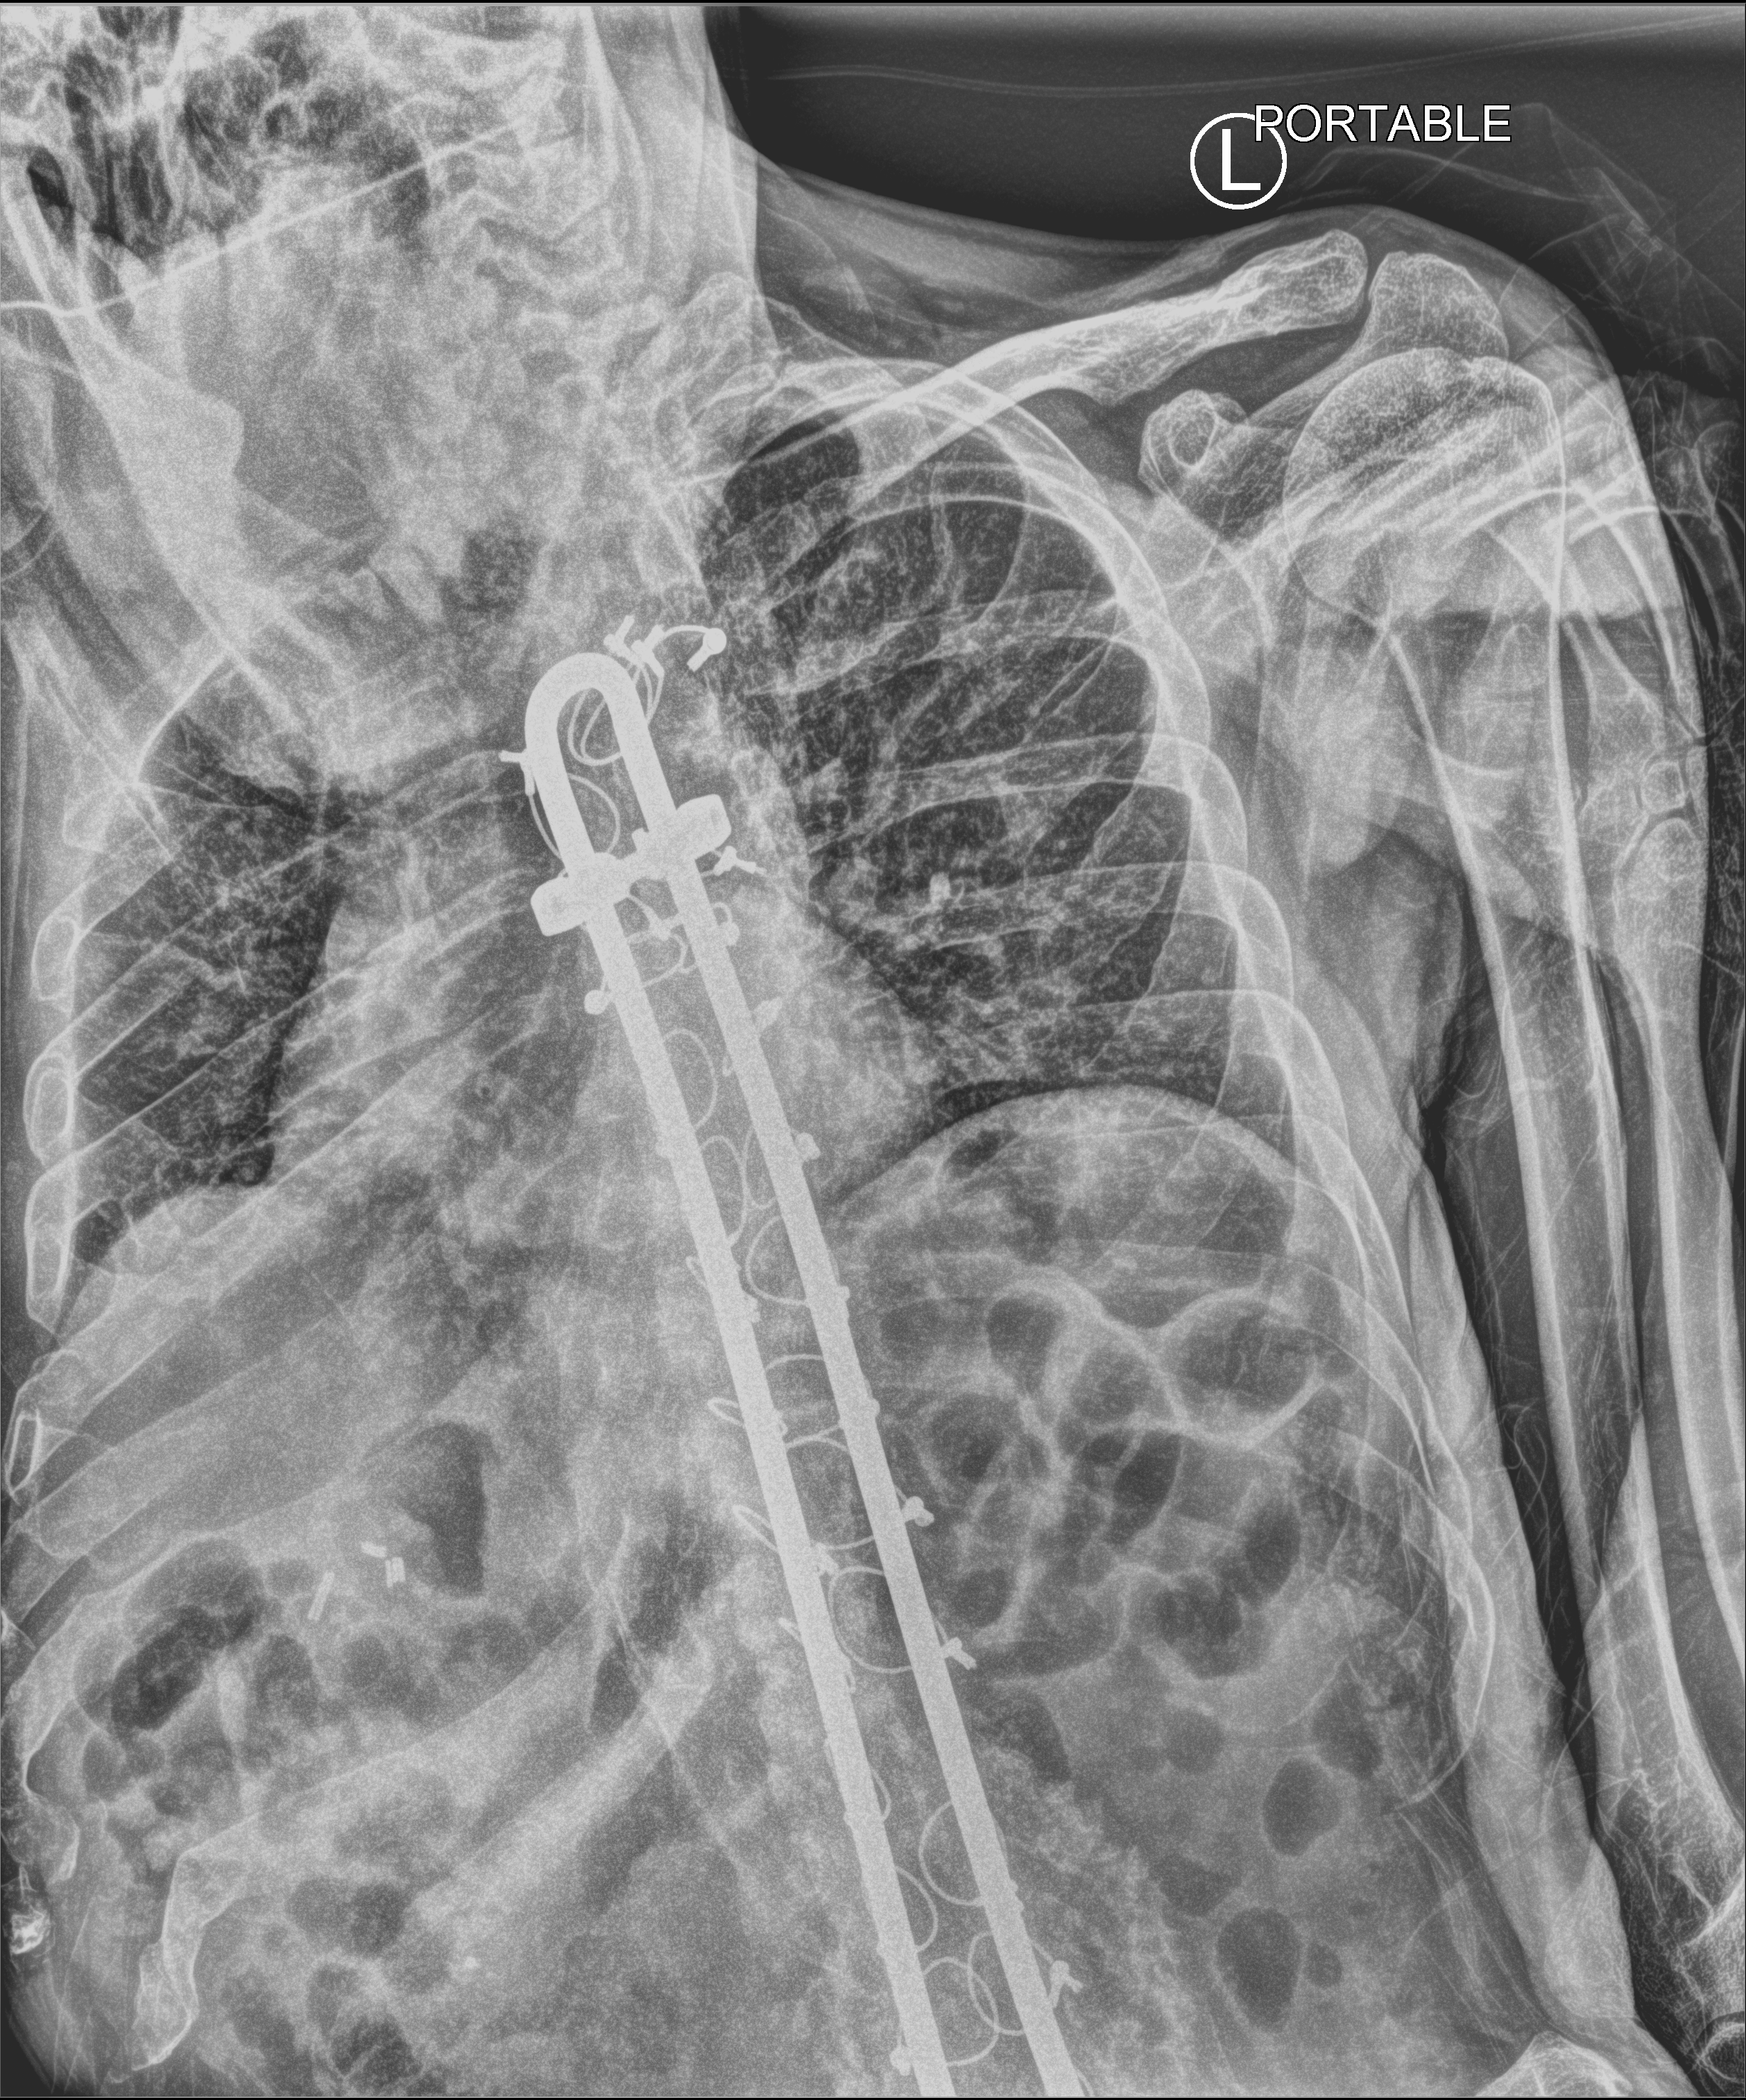
Bedside chest radiograph (computed radiography); anteroposterior (AP) projection. Patient hospitalised with COVID-19; male, aged 60–74 years.
From the hospital-stay record, not from the radiograph (when in the stay this image was taken is not recorded): admitted to intensive care during this hospital stay: no.